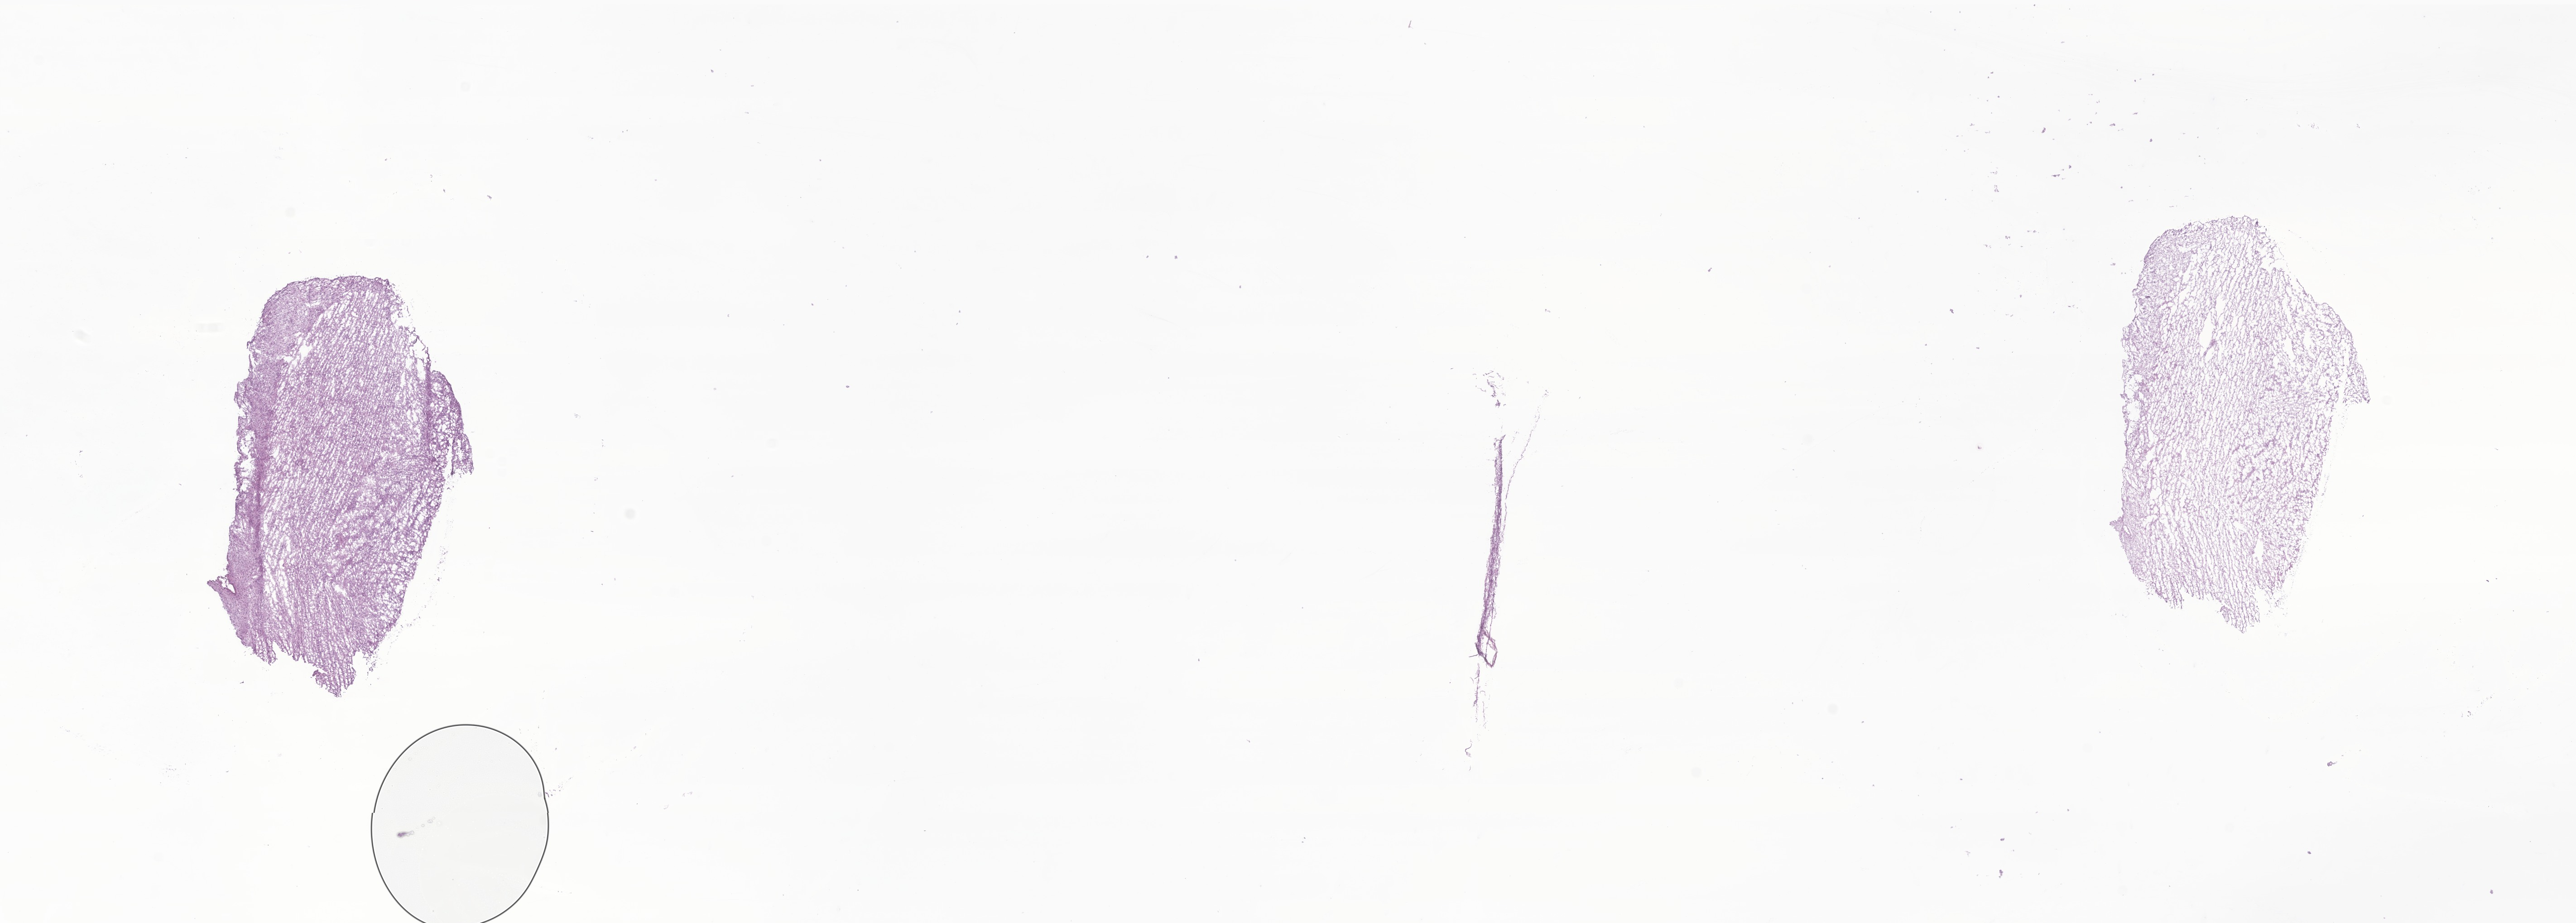
Digitized H&E-stained section of tumor tissue from the spinal cord — shown as a low-resolution overview of the whole scanned area (about 24.0 x 8.6 mm), frozen section. Patient: female, age 46 months (3 years 10 months).
Diagnosis (ICD-O-3 morphology term): Neoplasm, malignant.